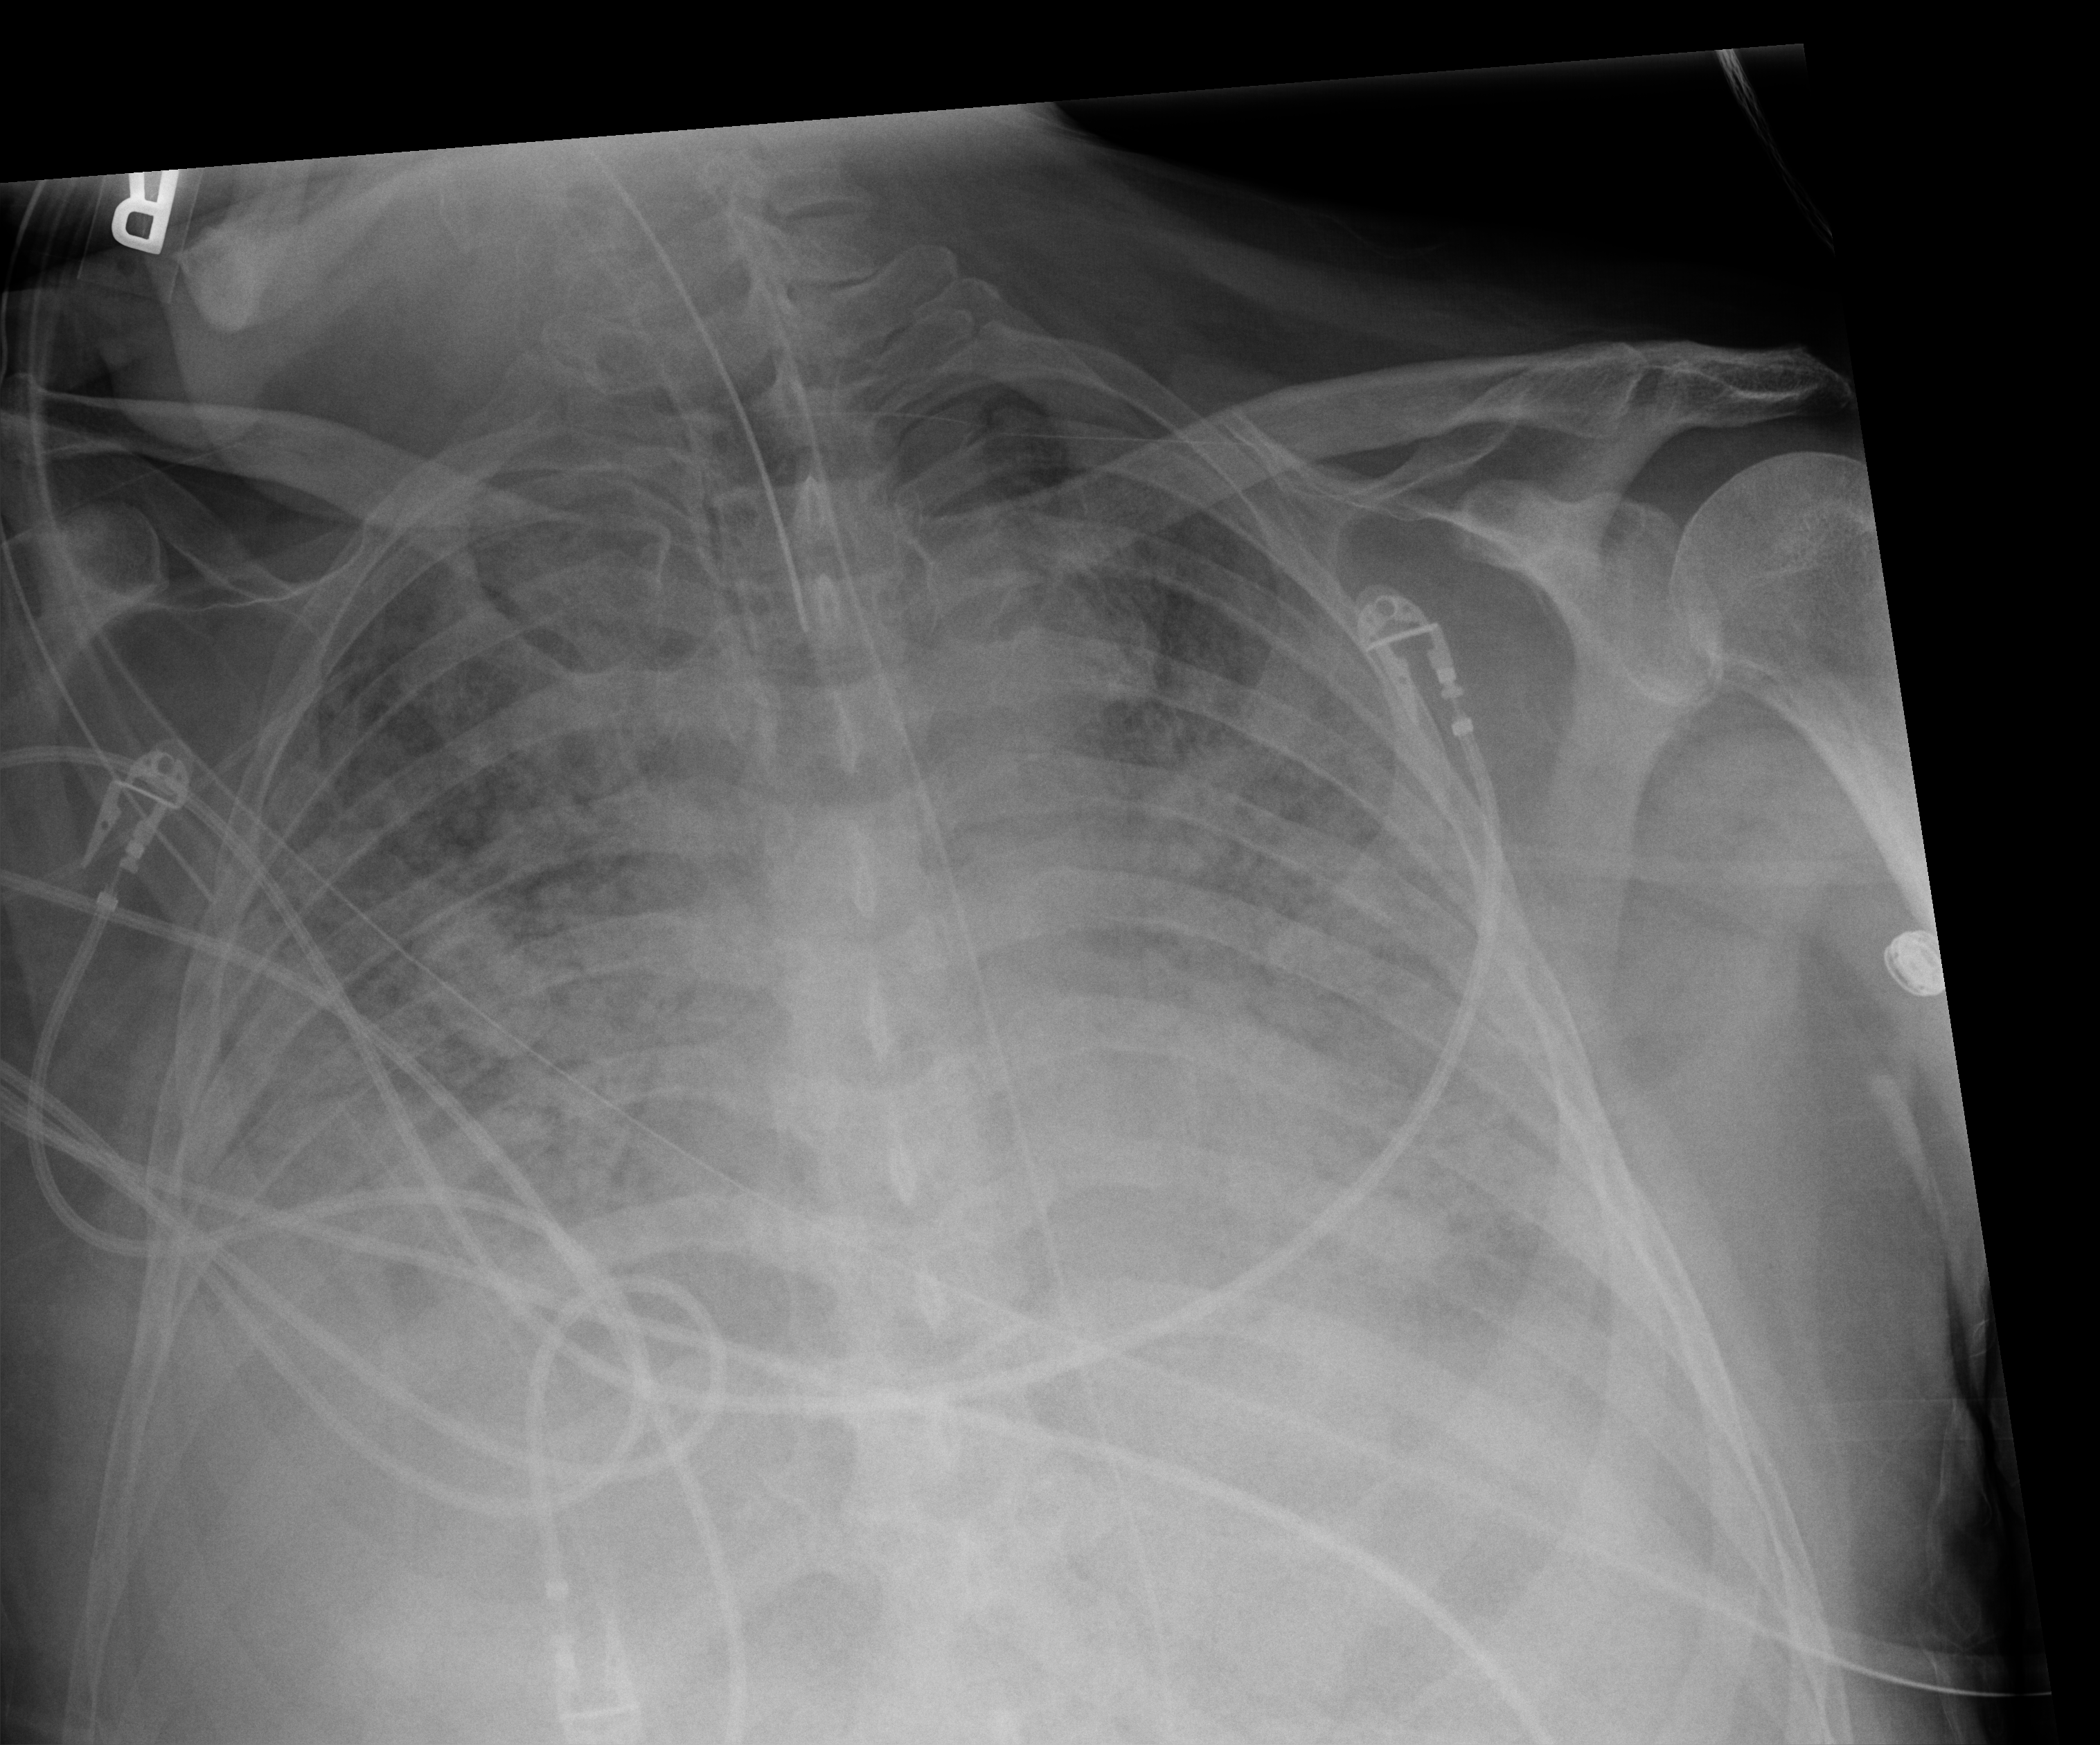
Portable chest radiograph; anteroposterior (AP) projection. Male patient hospitalised with COVID-19, age 60–74 years.
Admission-level facts for this patient (not findings on this image; timing relative to this image not recorded): smoking status (admission record): former; admitted to intensive care during this hospital stay: yes.